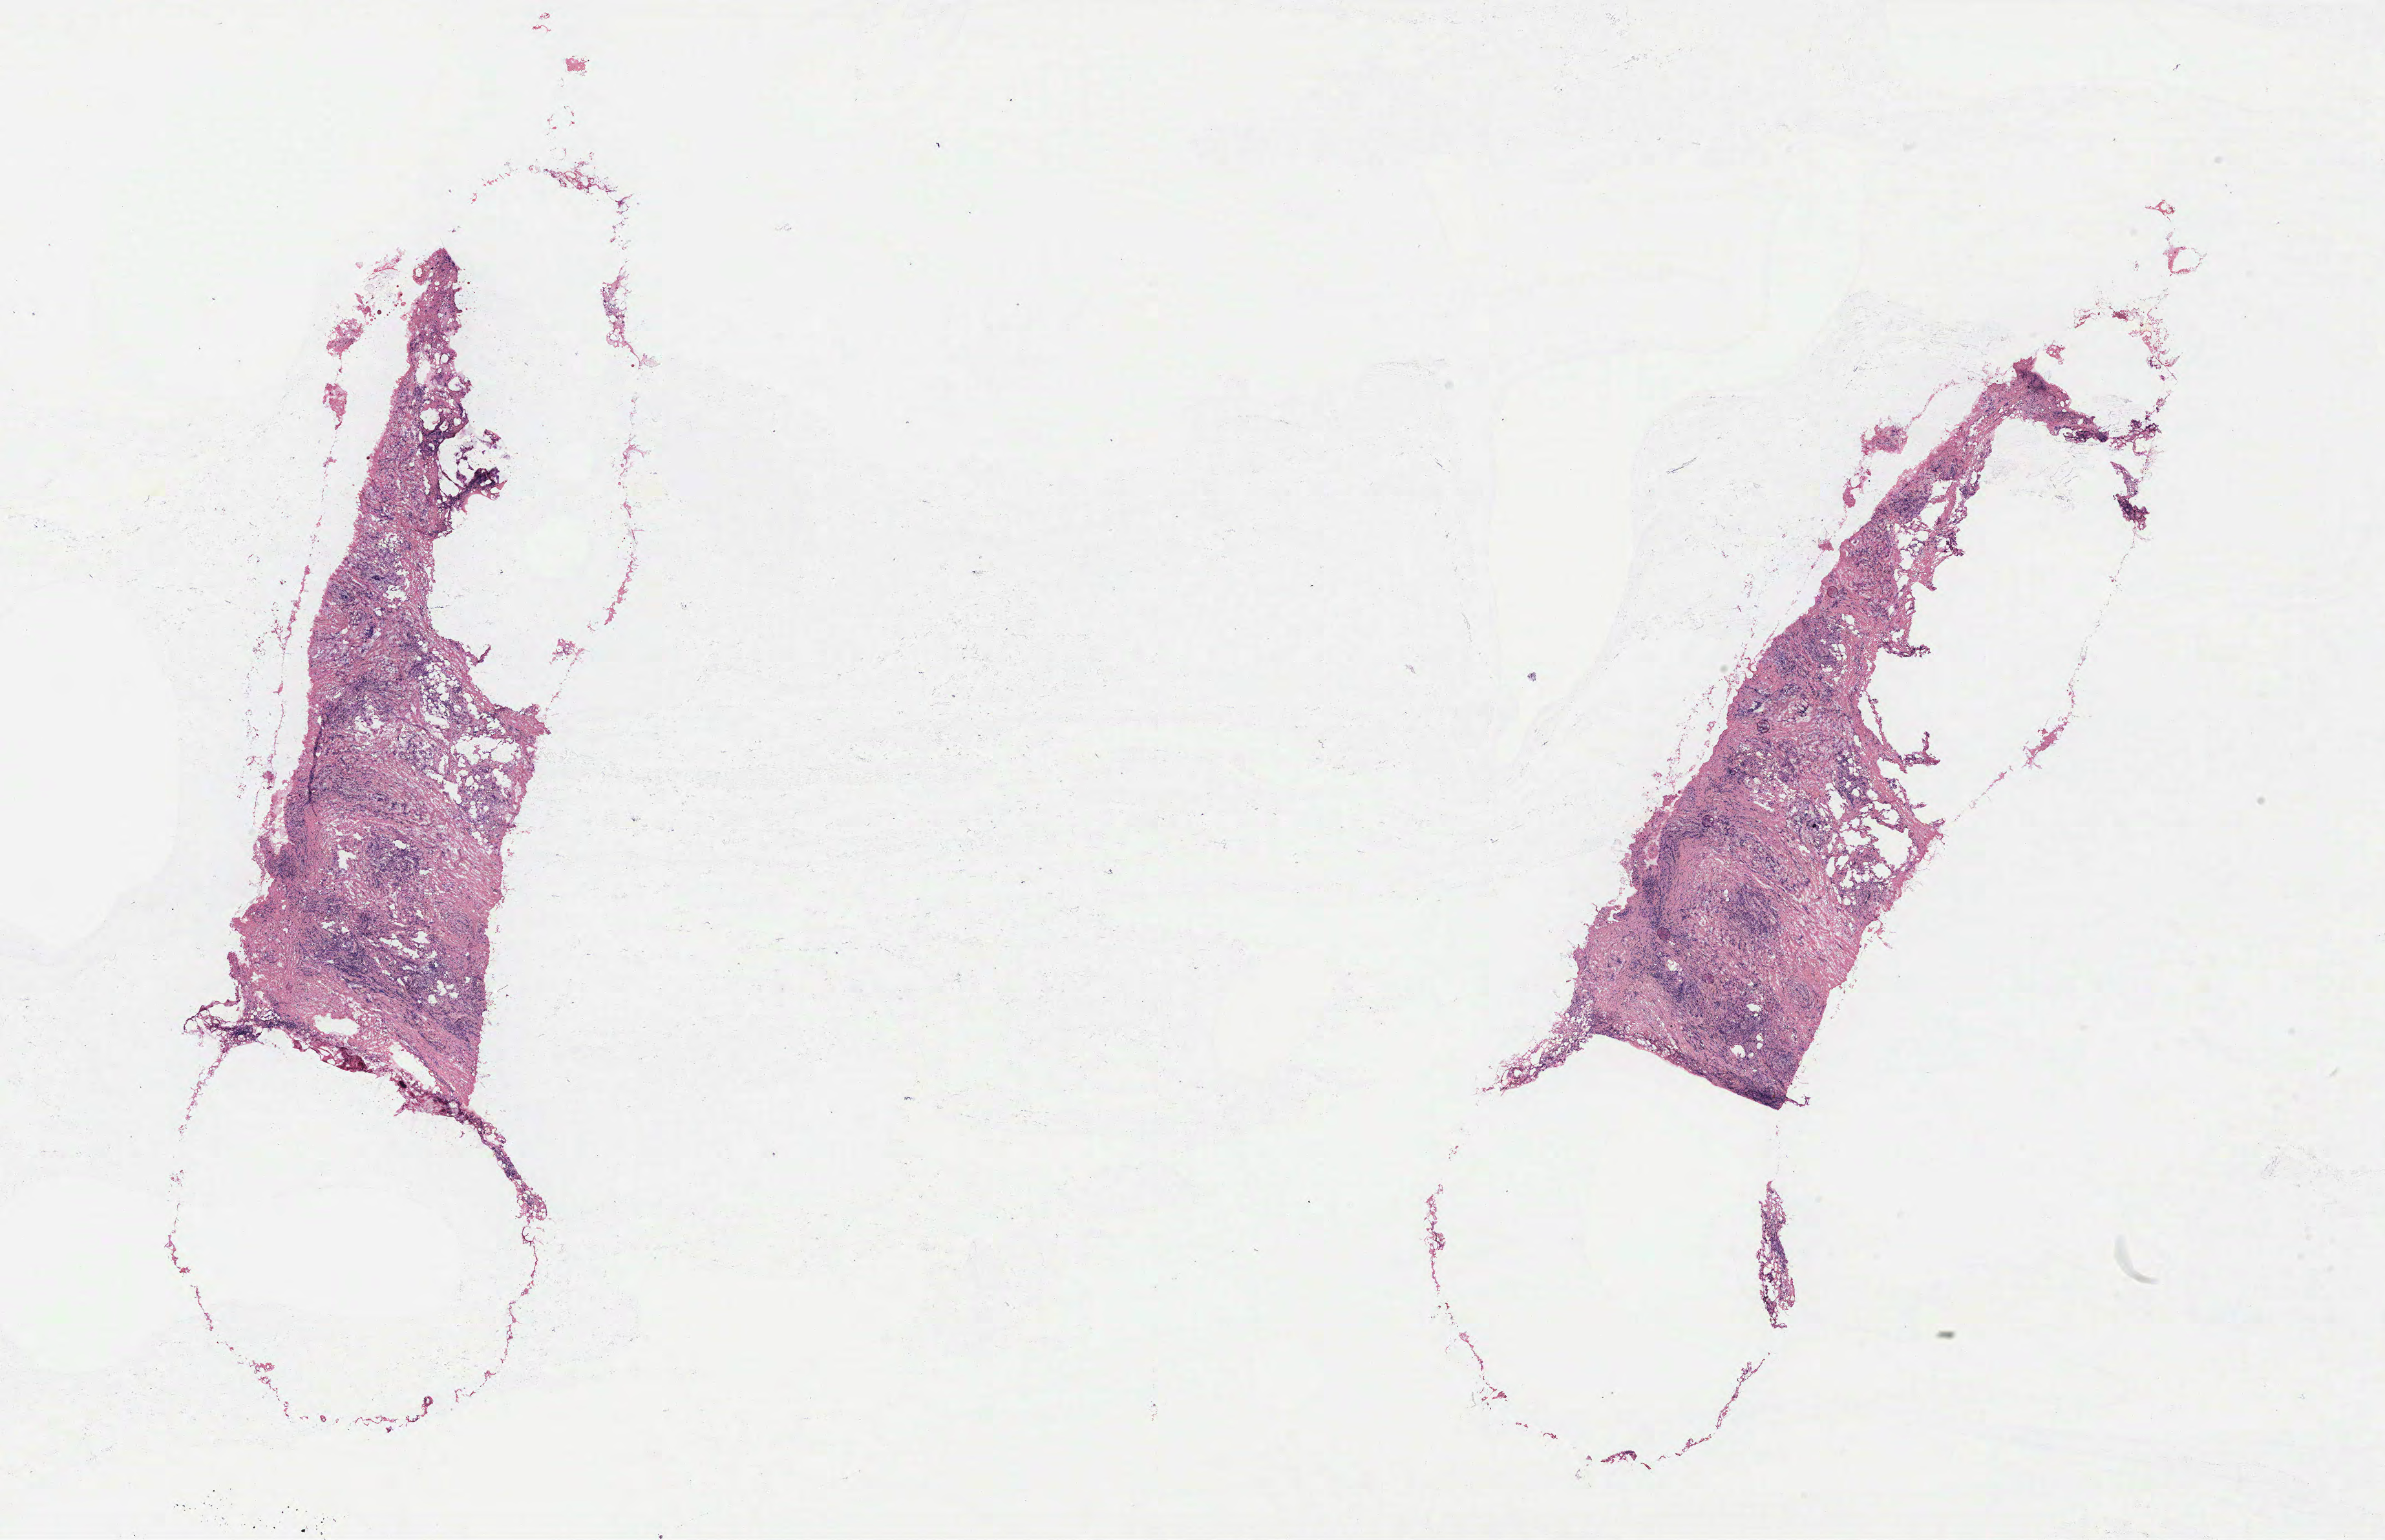
Digitized H&E tissue section (whole slide) — low-resolution overview of the scanned area, about 29.5 x 19.1 mm (slide scanned at 40x), breast, tissue type not recorded.
Patient diagnosis (cohort enrolment): breast cancer (breast).